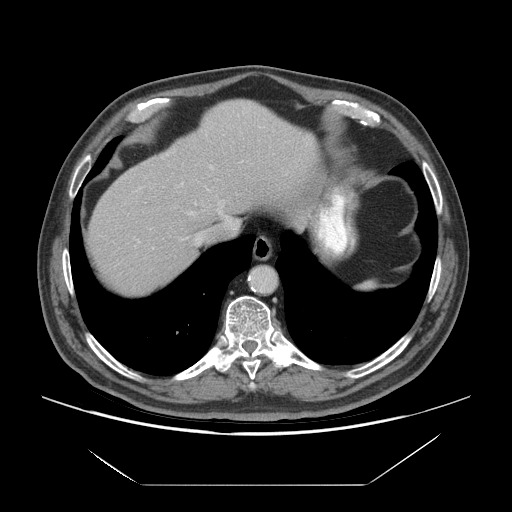
Contrast-enhanced abdominal CT (liver protocol), one axial slice; slice 60 of 75 in the series (ordered by position); reconstruction kernel STANDARD; soft-tissue window (W 400 / L 40 HU); 2.5 mm slice thickness; 512 × 512 image matrix, field of view 420 × 420 mm. Case-level facts recorded for this patient, not image findings: diagnosis: hepatocellular carcinoma (patient treated with transarterial chemoembolisation; whether this scan precedes or follows treatment is not stated here); TNM stage (as recorded): Stage-I; Child-Pugh class: A; tumour nodularity: uninodular.
Annotated regions visible in this slice (semi-automatically segmented with operator editing):
- abdominal aorta: bounding box (x1, y1, x2, y2) in pixels: (250, 267, 276, 292)
- liver parenchyma outside the tumour (the mass and vessels are separate outlines, so this box may not span the whole liver): (88, 100, 322, 294)
- liver vessels: (189, 166, 212, 241)